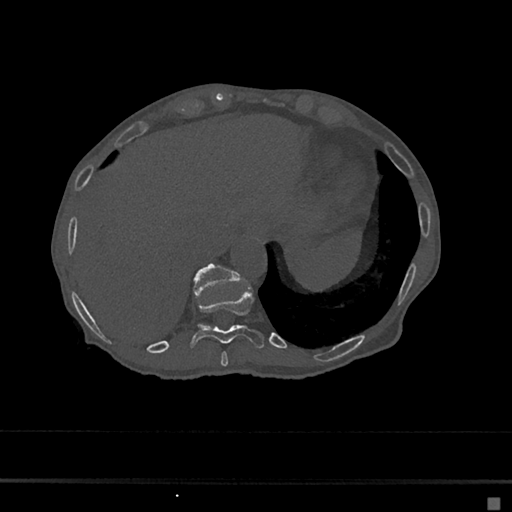
CT including the spine, one axial slice; reconstruction kernel Br40s/3; 120 kVp; bone window (W 1800 / L 400 HU); 512 × 512 image matrix, field of view 360 × 360 mm. Patient: female, 68 years. Case-level facts recorded for this patient, not image findings: primary cancer: renal.
Outlined on this slice (semi-automatically segmented with operator editing):
- T10 vertebra: bounding box (x1, y1, x2, y2) in pixels: (189, 287, 265, 350)
- T11 vertebra: (193, 263, 240, 296)
- T9 vertebra: (220, 351, 228, 367)